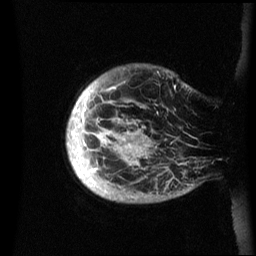
Breast MRI (dynamic contrast-enhanced), one sagittal slice; slice 4 of 60 in the series (ordered by position); dynamic contrast-enhanced series, image 2 of 3 at this slice position (ordered by acquisition); 1.5 T; TE 4.2 ms, TR 8.4 ms; 256 × 256 image matrix, field of view 230 × 230 mm. Patient: female, 48 years.
Annotated regions visible in this slice (semi-automatic segmentation, software-assisted and operator-edited):
- analysis volume of interest (the breast-tissue region the enhancement analysis was run in; not a lesion): bounding box (x1, y1, x2, y2) in pixels: (66, 64, 202, 203)
- tumour enhancement mask (voxels above the 70 % enhancement threshold inside the analysis volume of interest): (67, 87, 148, 171)